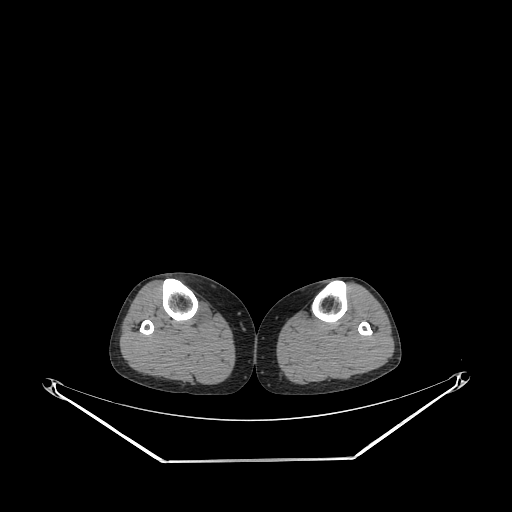
CT of an extremity soft-tissue mass (from a PET/CT study), one axial slice. Slice 152 of 267 in the series (ordered by position). Reconstruction kernel STANDARD. 140 kVp. Soft-tissue window (W 400 / L 40 HU). 3.75 mm slice thickness. 512 × 512 image matrix. Female patient. Case-level facts recorded for this patient, not image findings: histological type: undifferentiated – high grade; grade: high; site of the primary tumour: right thigh.
Structures marked on this image (expert contour drawn on MRI and transferred to this co-registered scan by the dataset authors):
- gross tumour volume (mass): box from (x=196, y=301) to (x=213, y=325) px